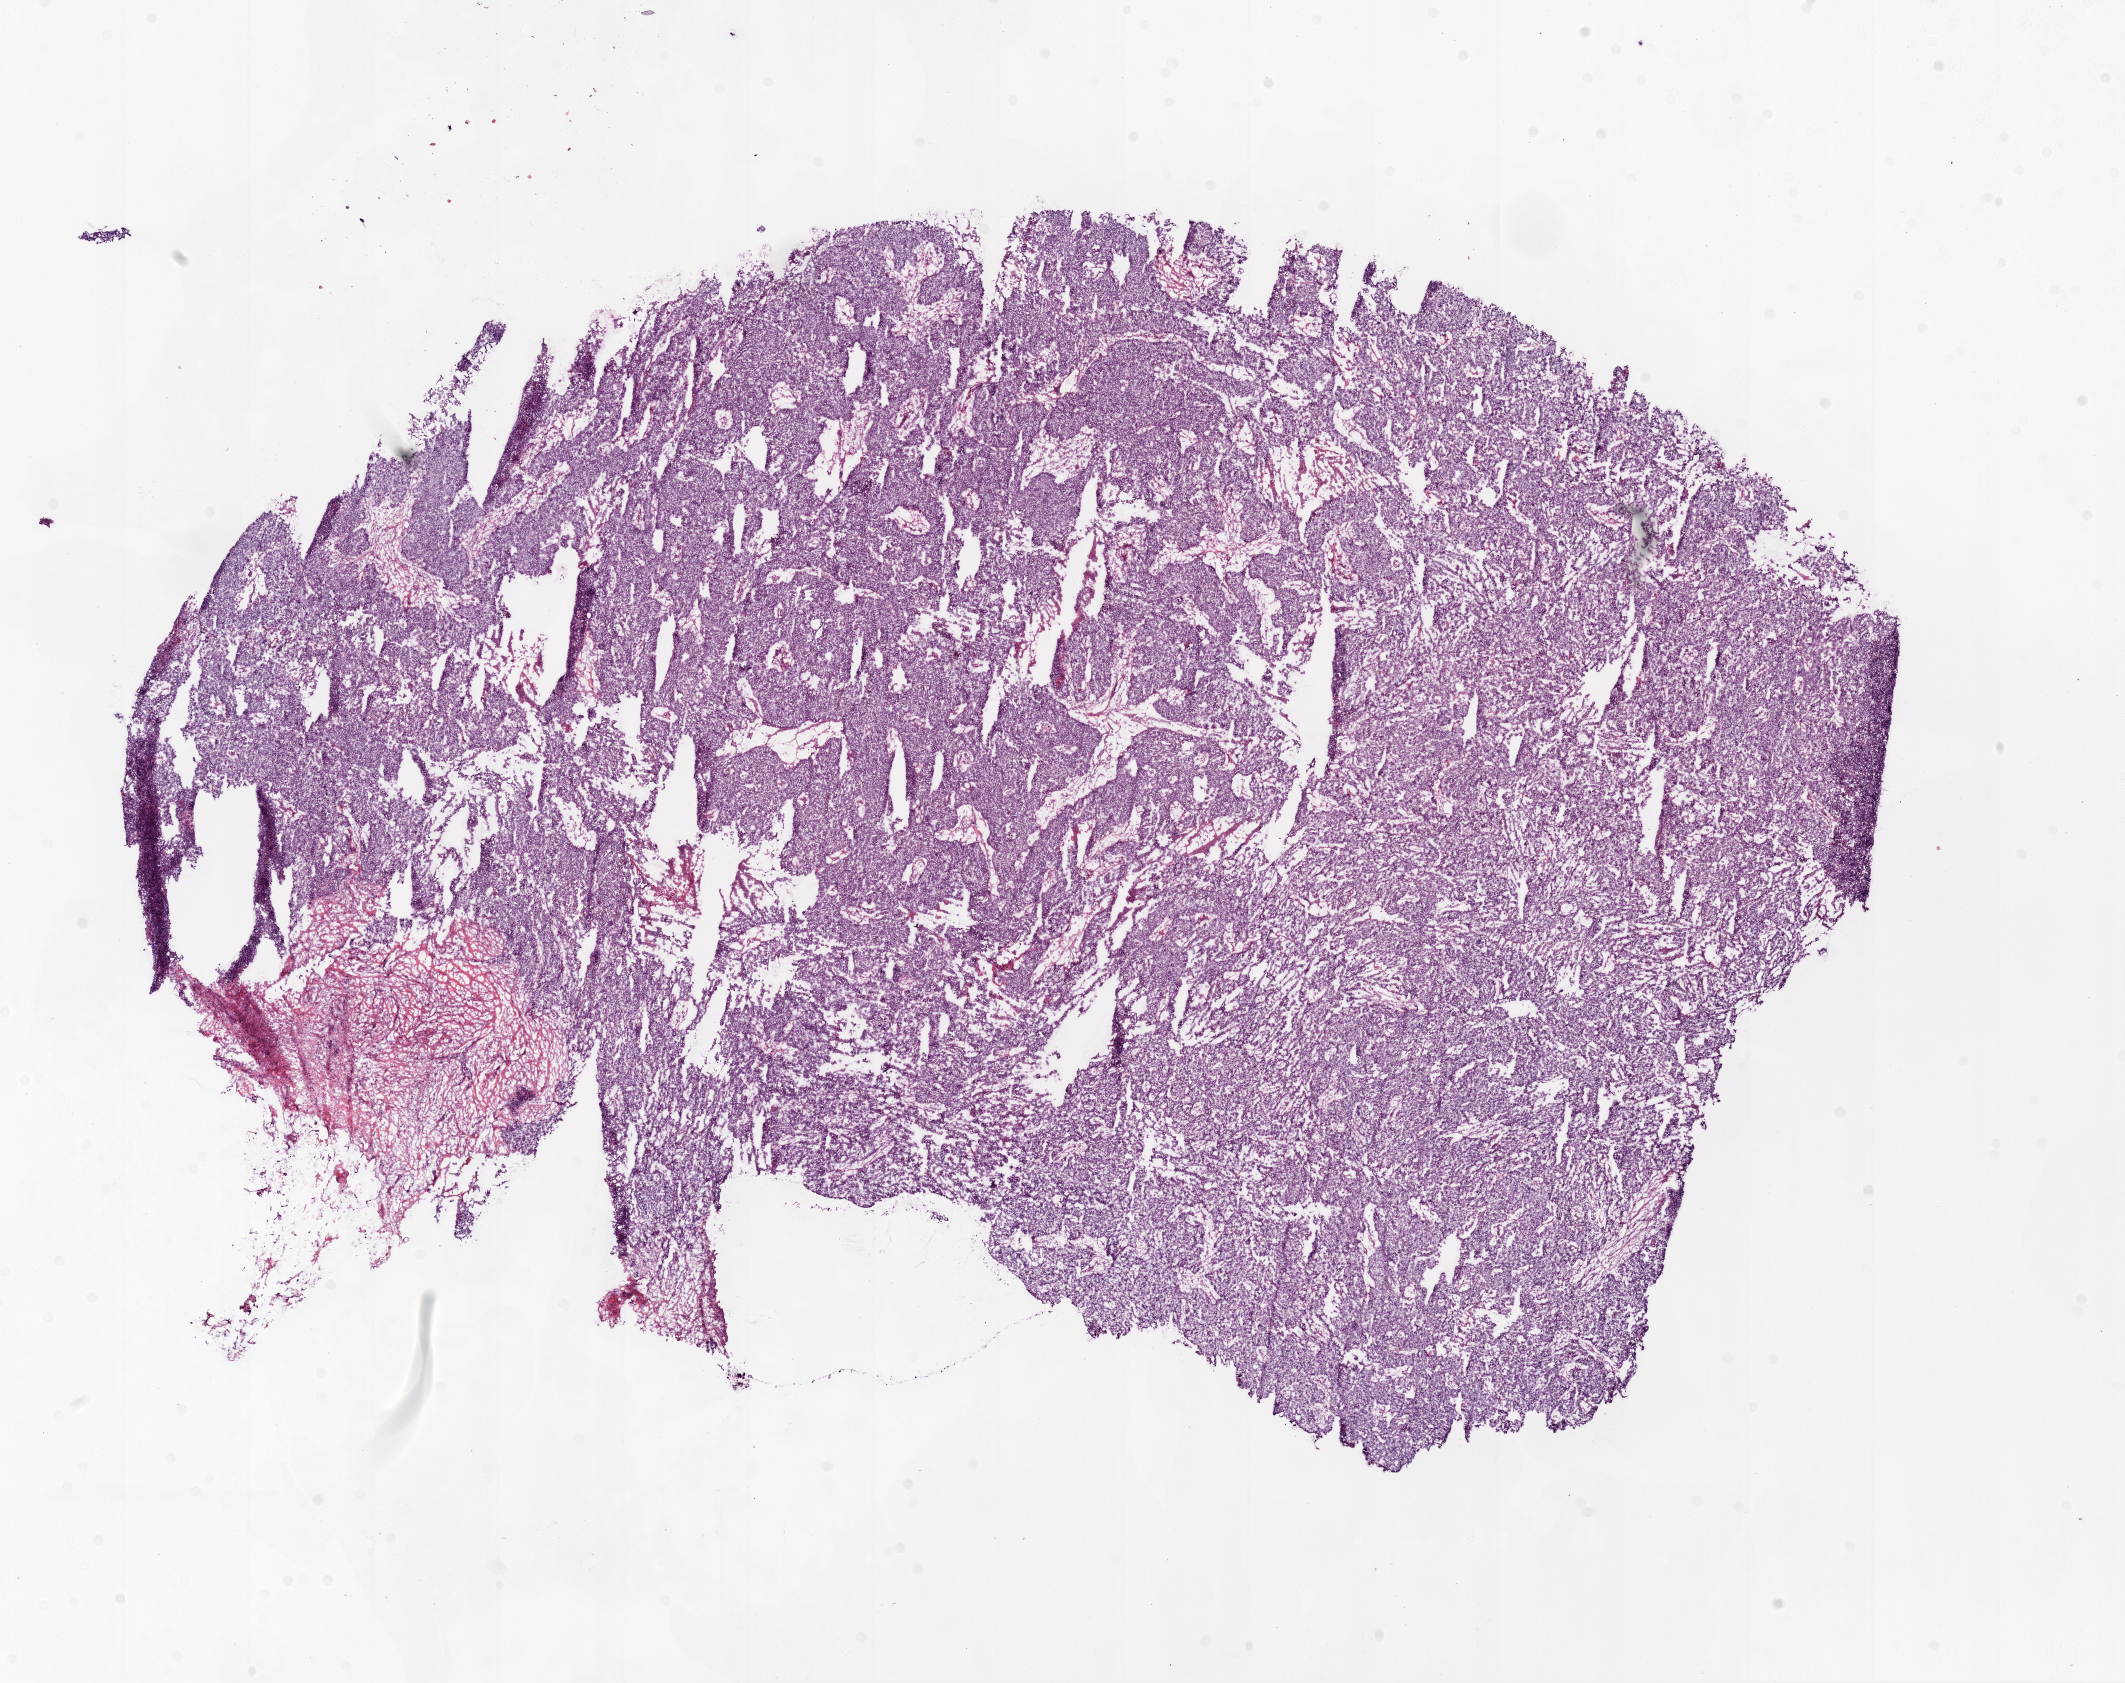
Whole-slide histology image, Hematoxylin and eosin (H&E) stained, whole scanned area (about 17.1 x 13.5 mm) shown as a low-resolution overview; frozen section from the bottom of the tissue portion; ovary, primary tumour sample. Female, age 56 years at initial diagnosis. Histologic grade: G3 (poorly differentiated). Slide review estimates, as recorded: tumour cells 90%, tumour nuclei 95%, normal cells 0%, stromal cells 5%, necrosis 5%.
* pathologic diagnosis: Serous cystadenocarcinoma, NOS (specified parts of peritoneum)
* FIGO stage: IIIC